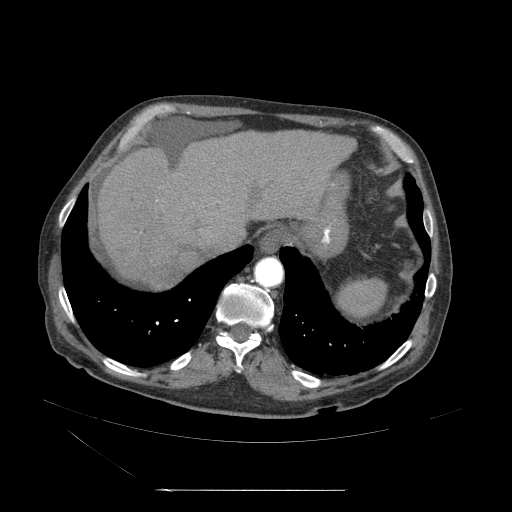
Contrast-enhanced abdominal CT (liver protocol), one axial slice. Slice 47 of 71 in the series (ordered by position). 120 kVp. Soft-tissue window (W 400 / L 40 HU). 2.5 mm slice thickness. 512 × 512 image matrix, field of view 440 × 440 mm. Case-level facts recorded for this patient, not image findings: diagnosis: hepatocellular carcinoma (patient treated with transarterial chemoembolisation; whether this scan precedes or follows treatment is not stated here); TNM stage (as recorded): Stage-II.
Annotated regions visible in this slice (semi-automatically segmented with operator editing):
- abdominal aorta: bounding box <254,256,285,289> (left, top, right, bottom; pixels)
- liver parenchyma outside the tumour (the mass and vessels are separate outlines, so this box may not span the whole liver): <96,132,347,288>
- mass: <145,270,183,299>
- liver vessels: <104,198,237,261>